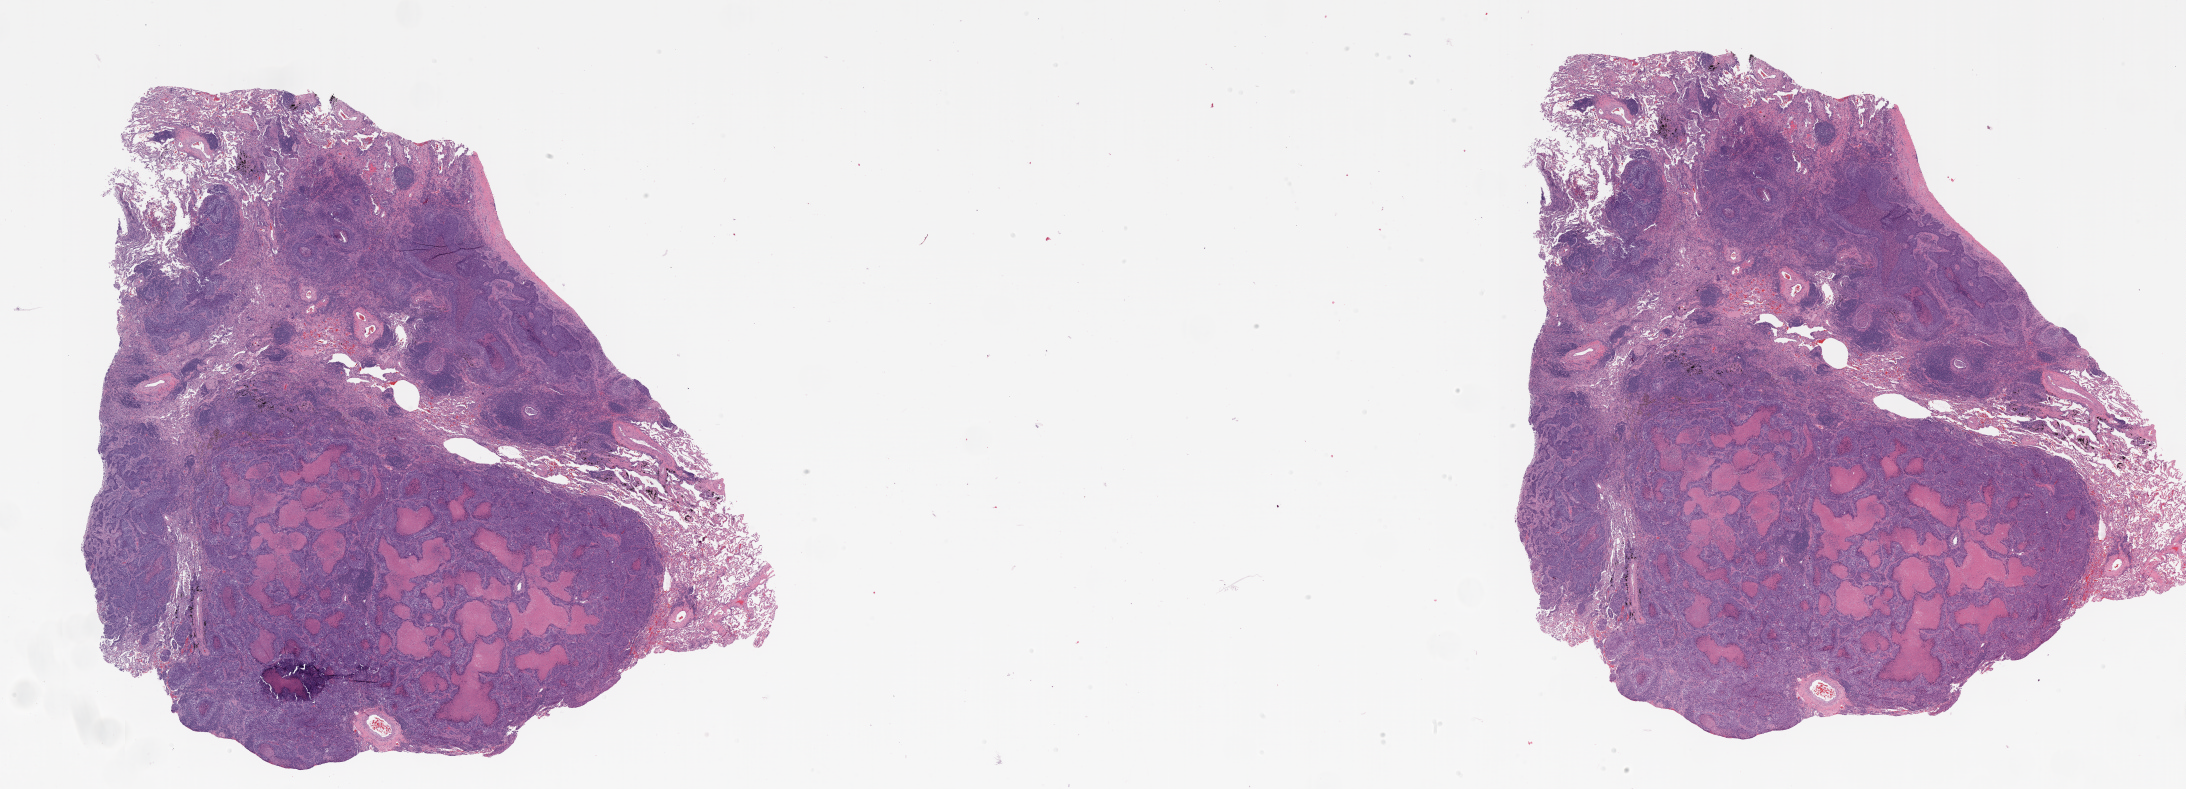
H&E whole-slide image — whole scanned area (about 35.0 x 12.6 mm) shown as a low-resolution overview; formalin-fixed paraffin-embedded (FFPE) diagnostic section; lung, primary tumour sample. Male patient.
Laterality: left. AJCC pathologic stage: IIA. TNM: T1 N1 M0. Pathologic diagnosis: Squamous cell carcinoma, NOS (lower lobe, lung).